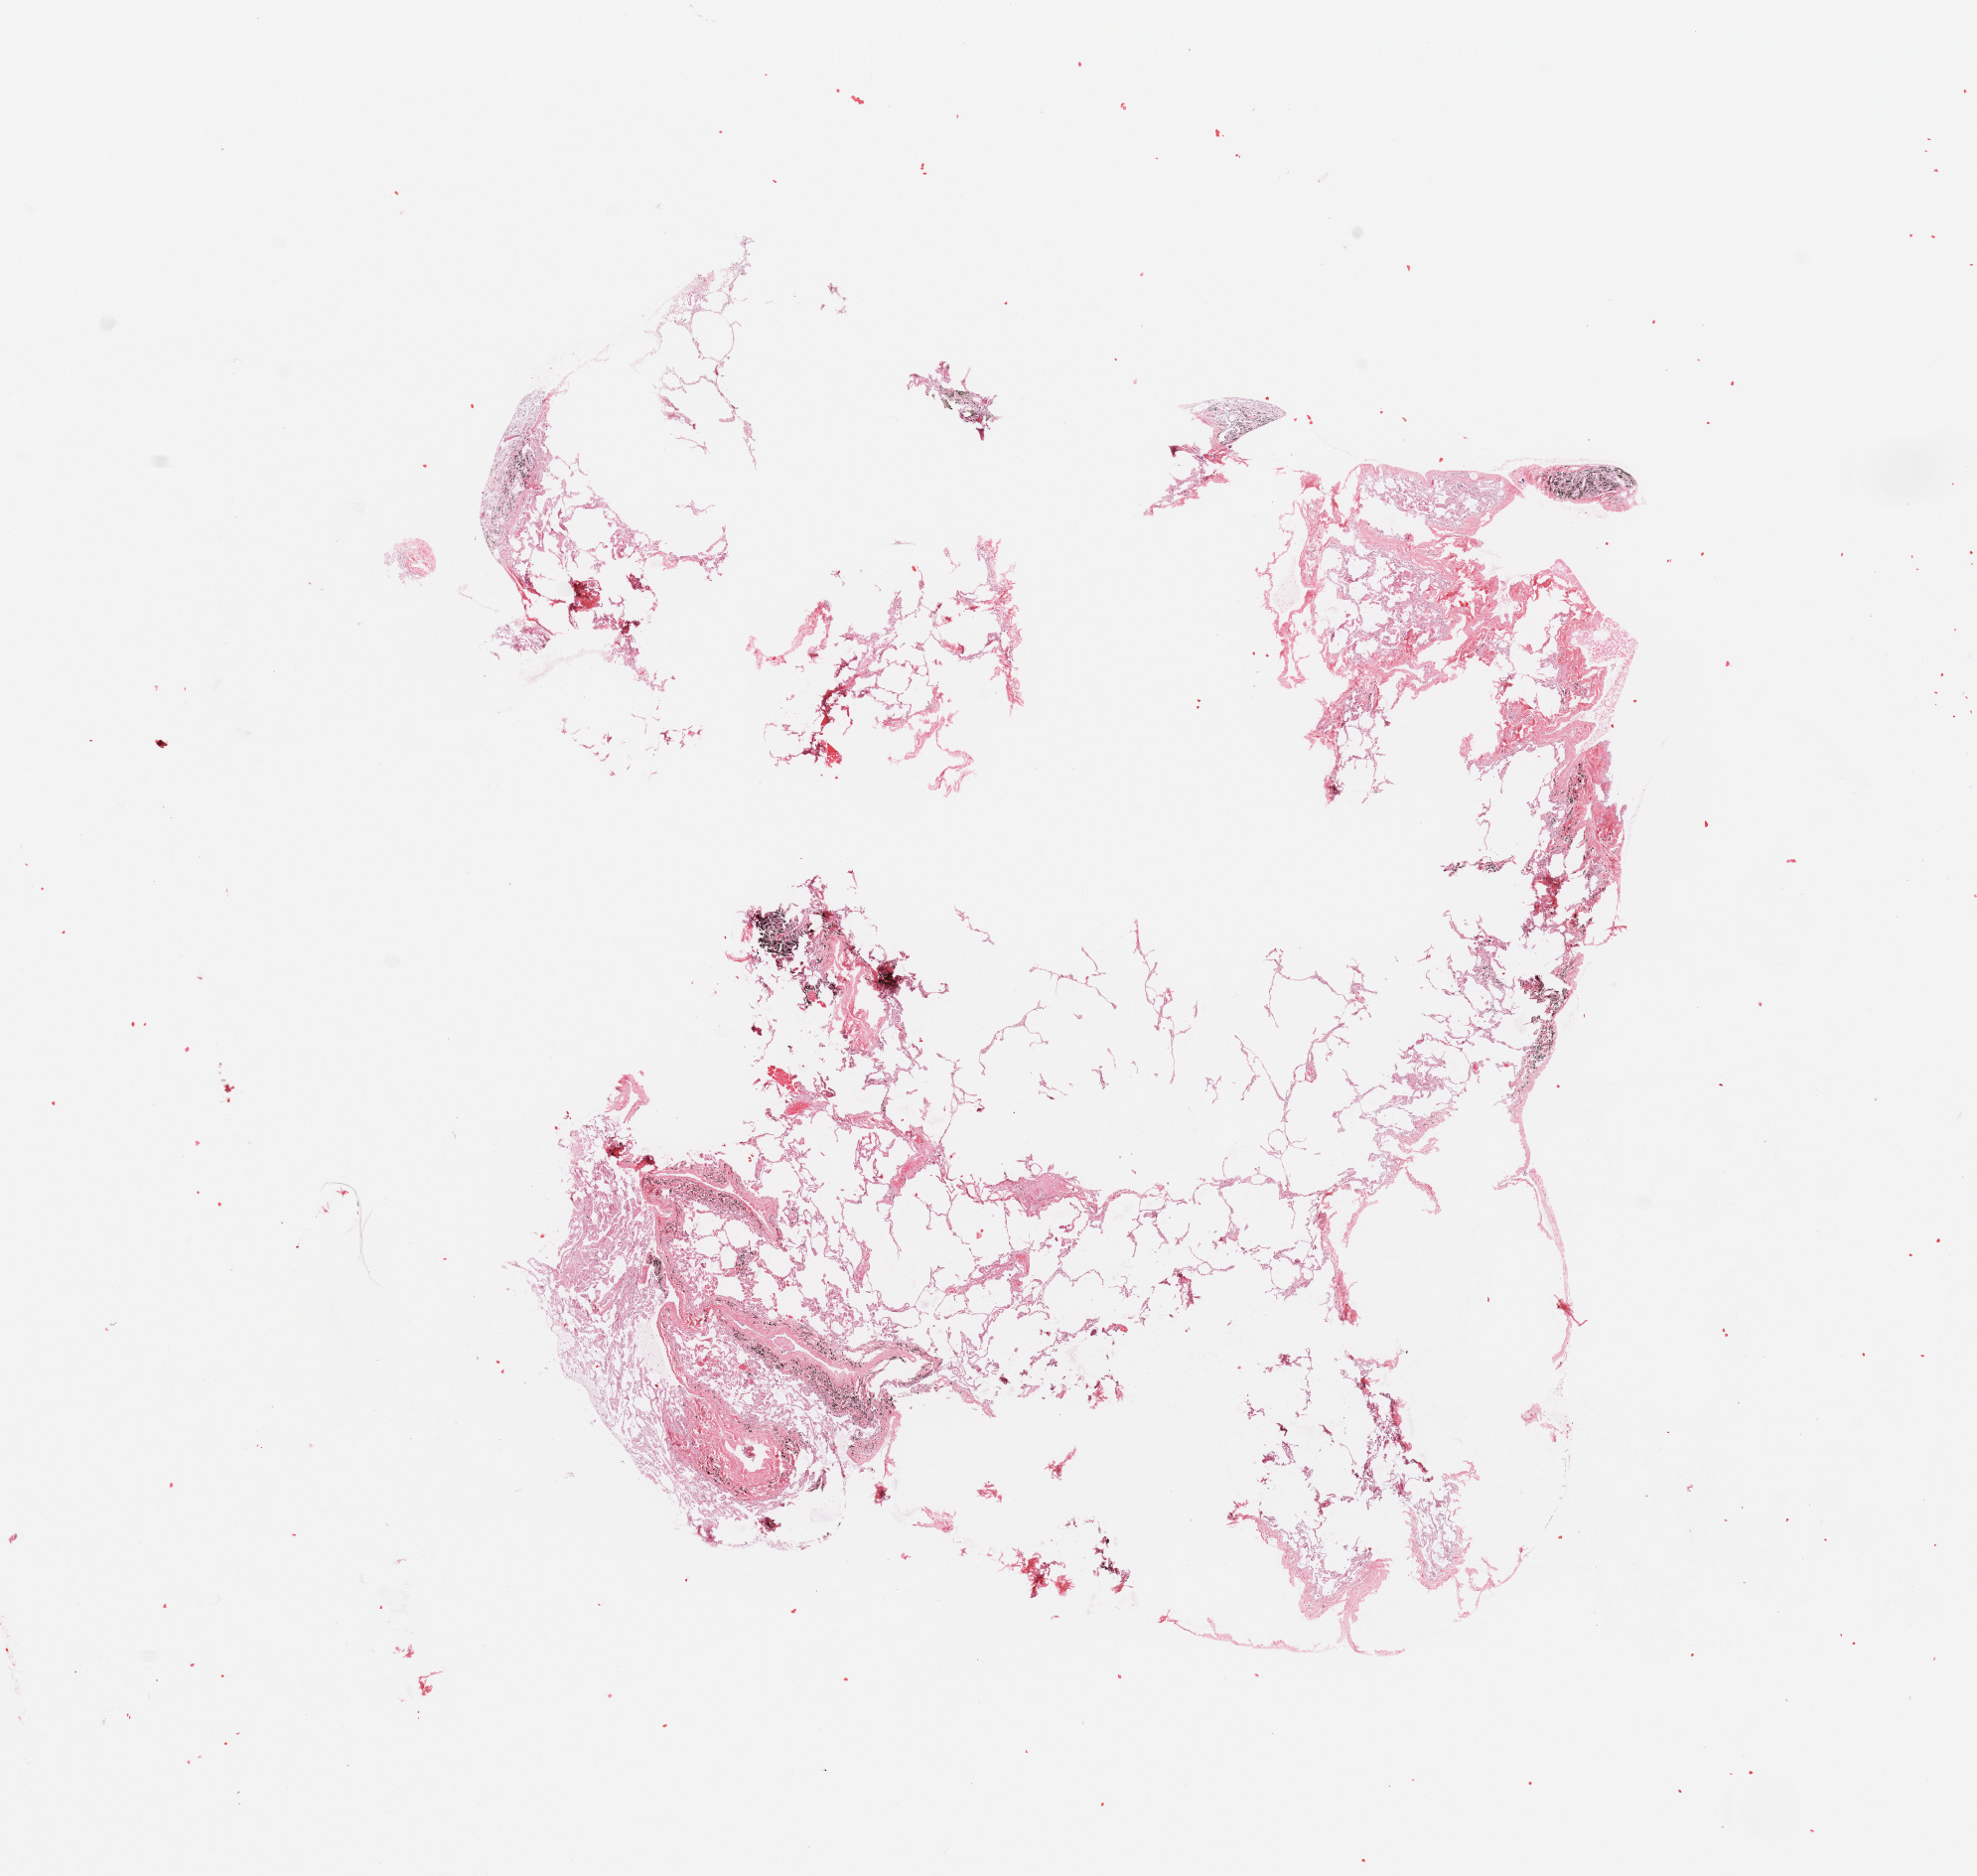
Digitized H&E tissue section (whole slide), whole scanned area (about 15.8 x 14.9 mm, slide scanned at 20x) shown as a low-resolution overview. Normal (non-tumour) tissue sample, sampled site: lung. Patient: female, age 56 years.
- this section: normal (non-tumour) tissue from the same patient
- patient diagnosis: Squamous cell carcinoma, NOS